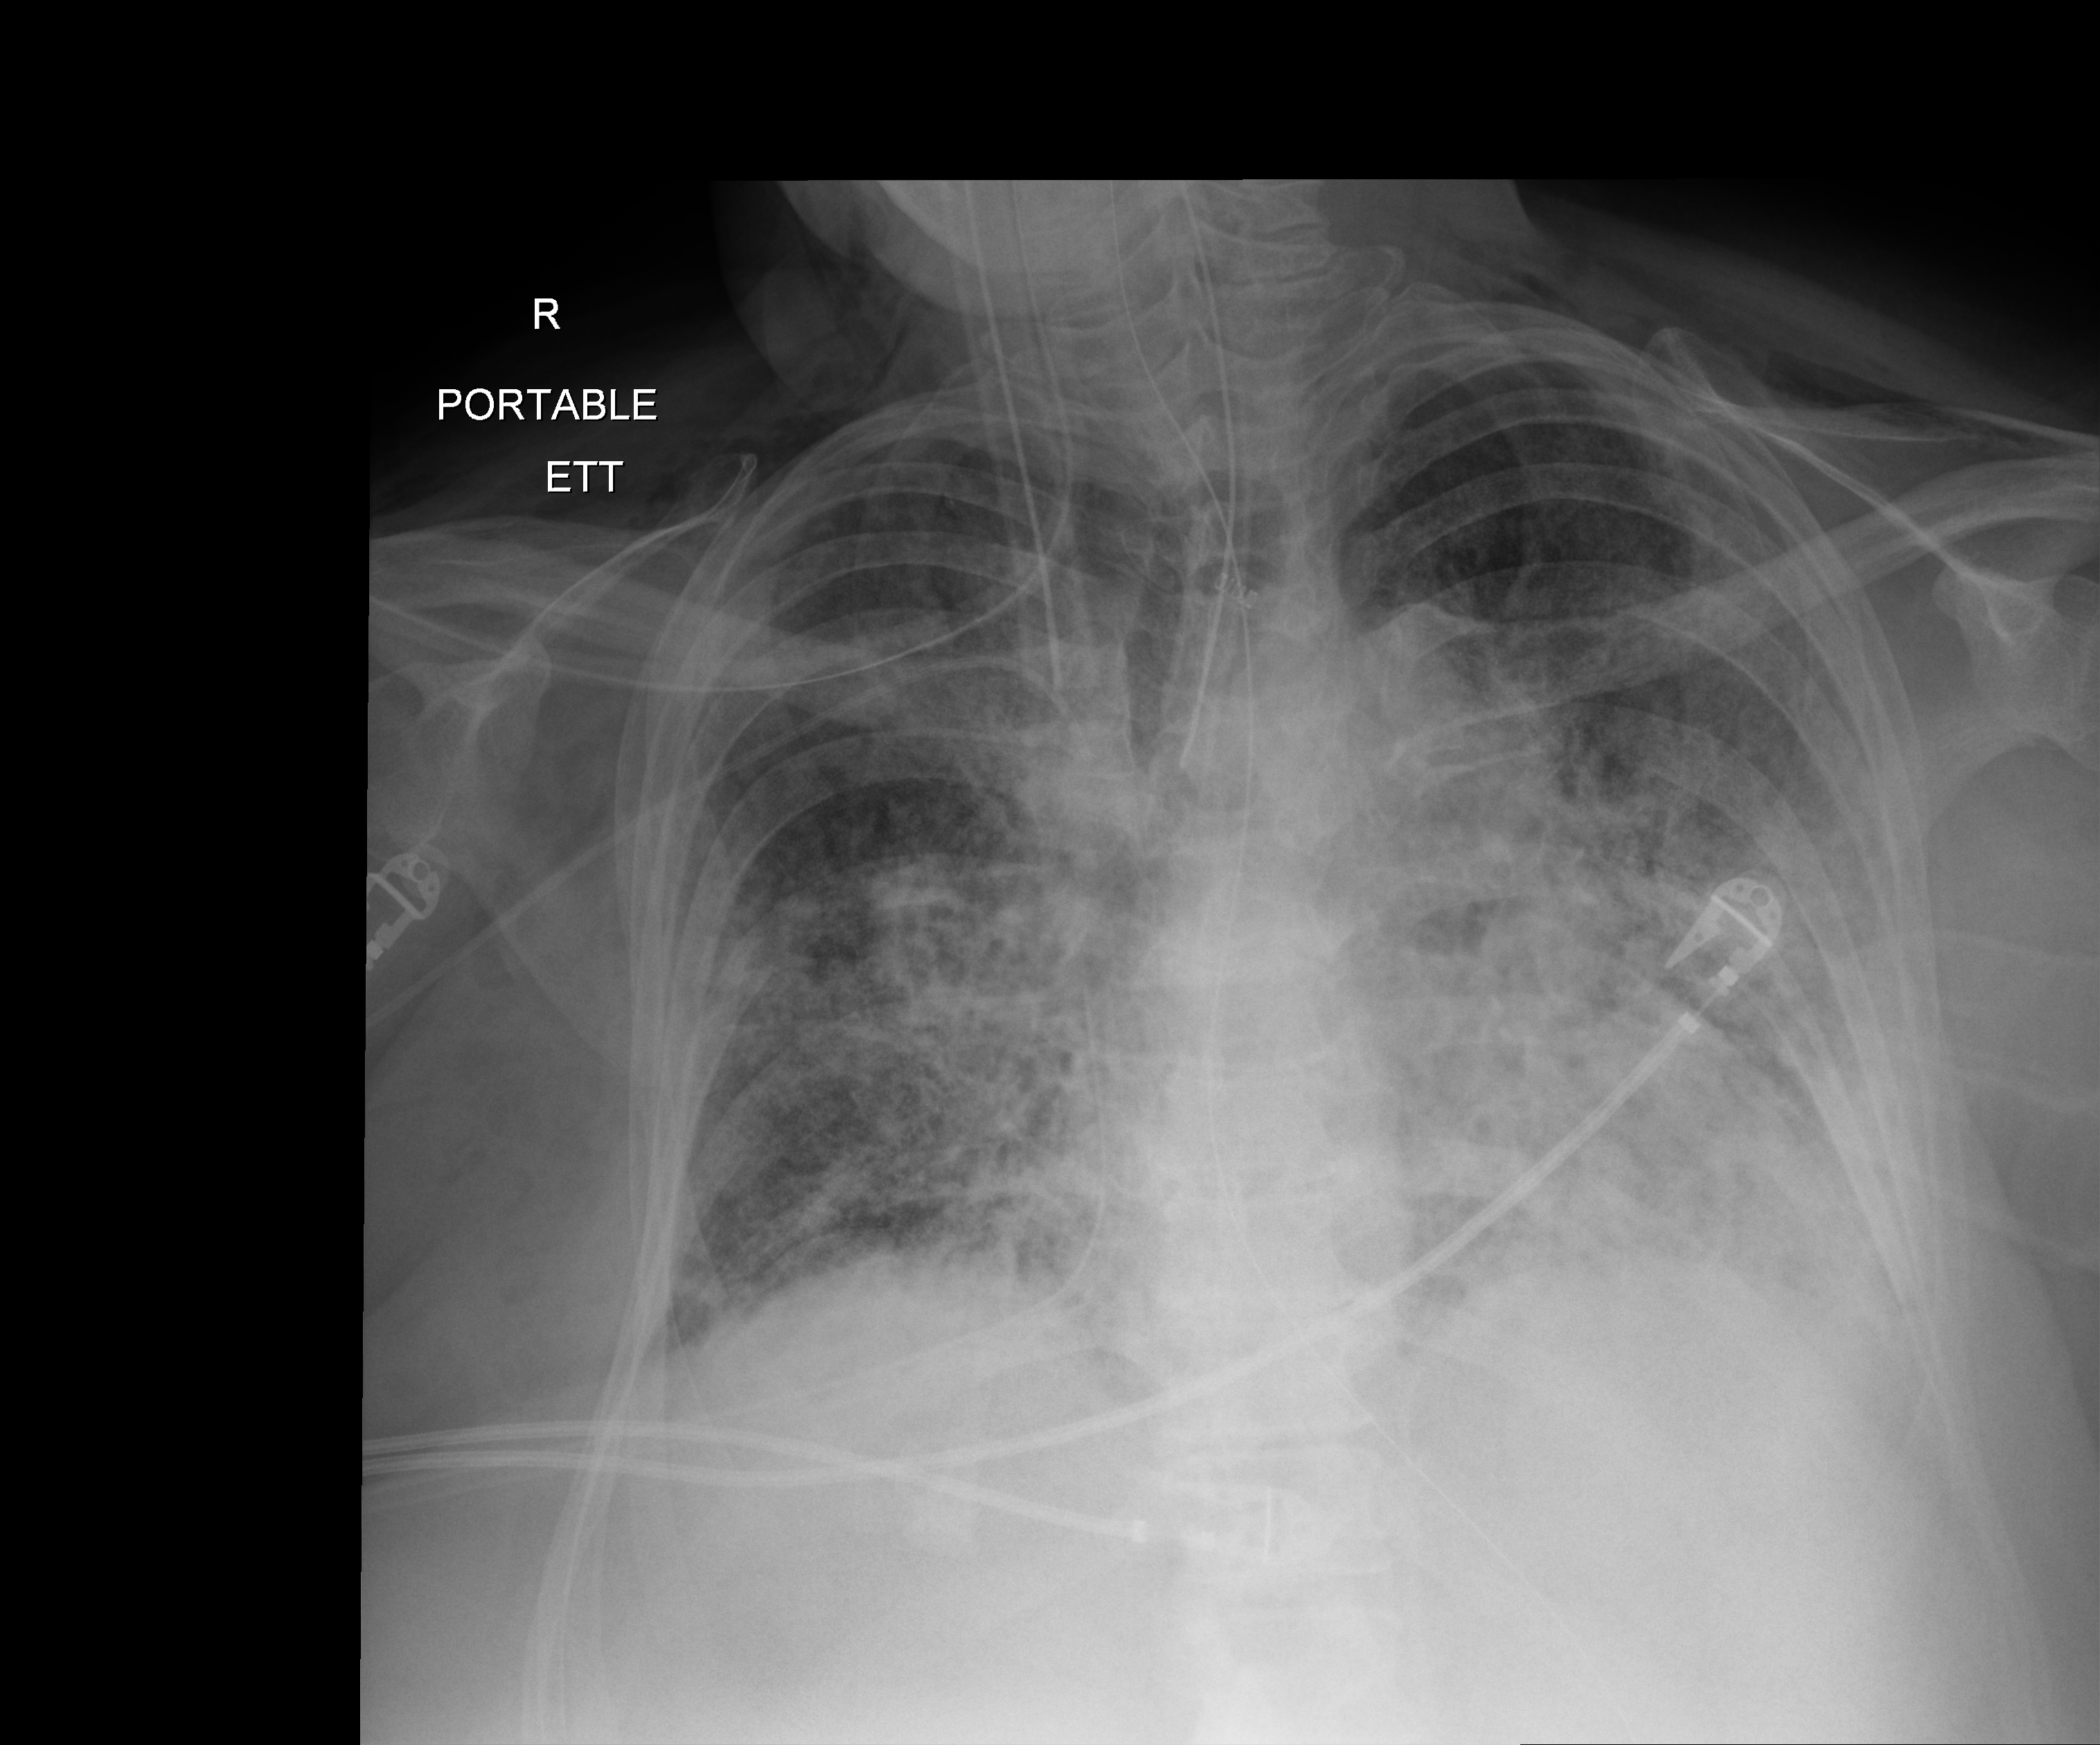
Chest X-ray; anteroposterior (AP) projection. Female patient hospitalised with COVID-19, age 60–74 years.
Admission-level facts for this patient (not findings on this image; timing relative to this image not recorded): mechanically ventilated during this hospital stay: yes.